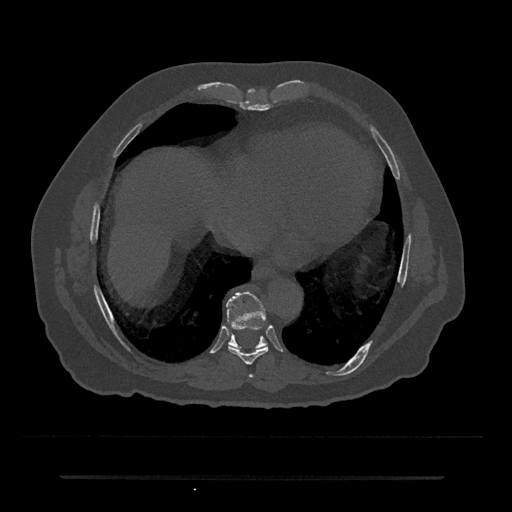
CT including the spine, one axial slice; slice 311 of 797 in the series (ordered by position); 120 kVp; bone window (W 1800 / L 400 HU); 0.5 mm slice thickness; 512 × 512 image matrix. Patient: male, 69 years. Case-level facts recorded for this patient, not image findings: primary cancer: prostate.
Annotated regions visible in this slice (semi-automatically segmented with operator editing):
- T7 vertebra: box from (x=249, y=375) to (x=253, y=378) px
- T8 vertebra: (x=228, y=345)–(x=268, y=365)
- T9 vertebra: (x=226, y=291)–(x=267, y=348)